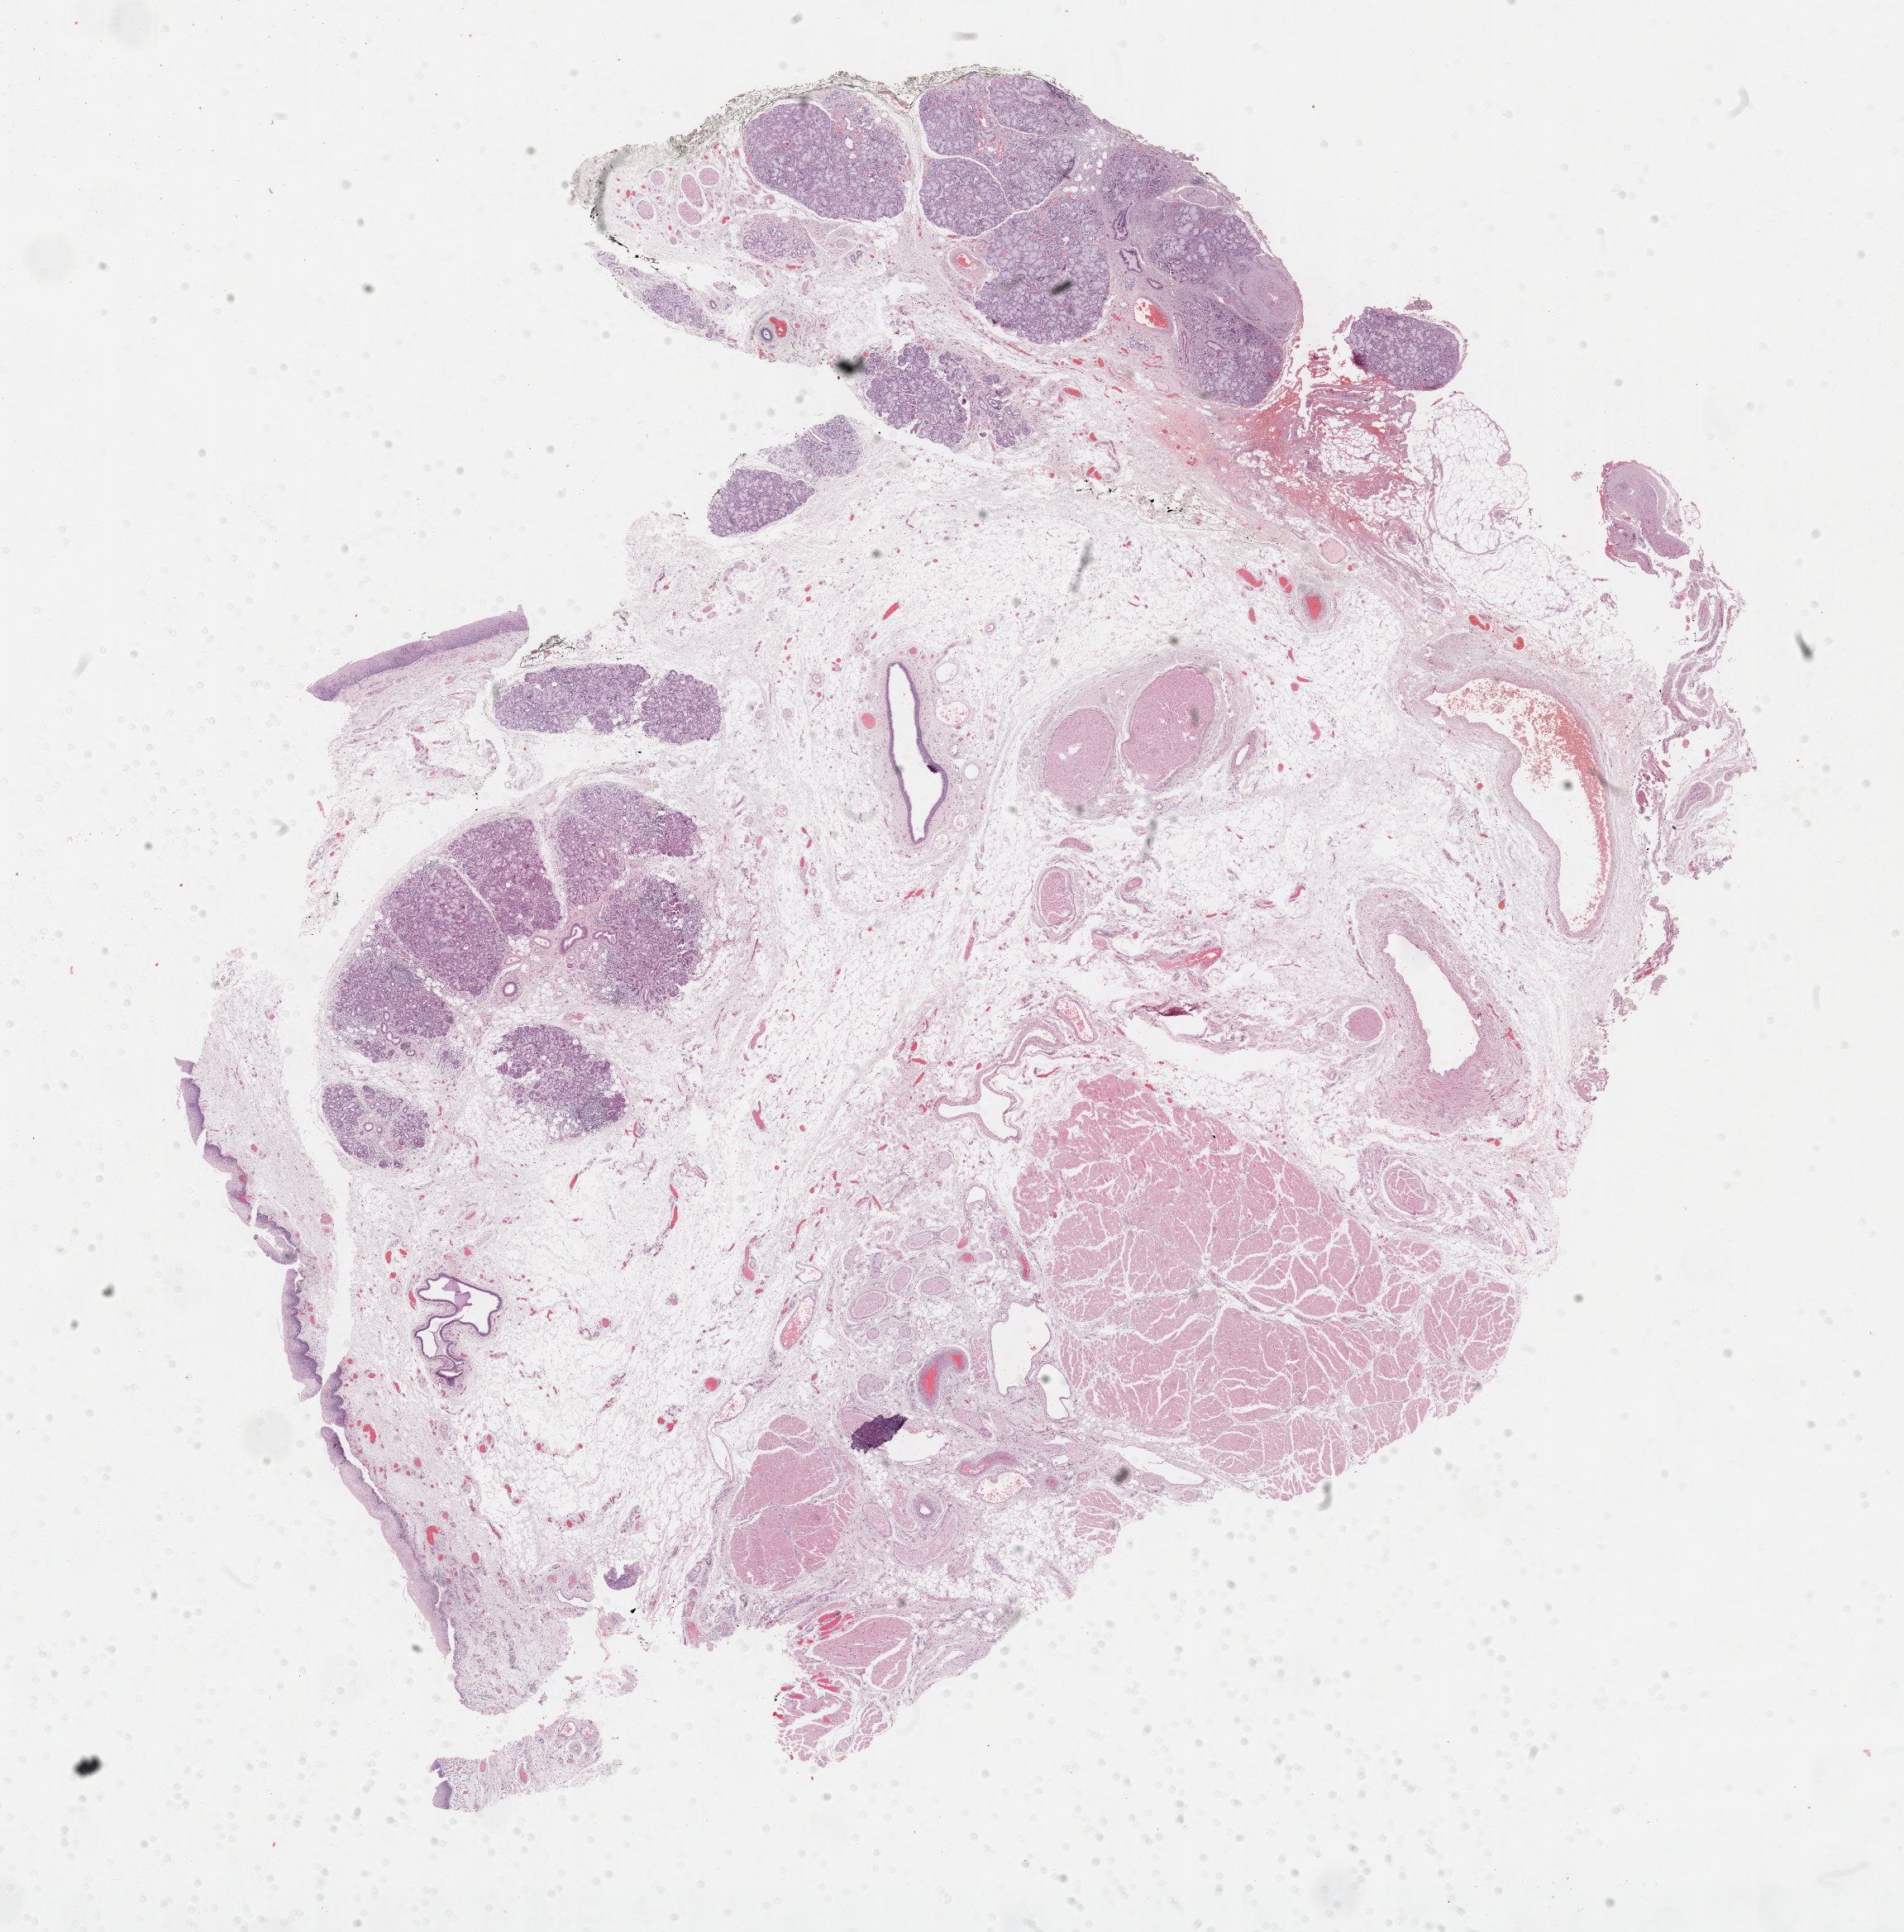
Hematoxylin and eosin (H&E) stained whole-slide image, shown as a low-resolution overview of the whole scanned area (about 18.6 x 18.9 mm); FFPE section; head and neck, primary tumour sample. Female patient; age at initial diagnosis 65 years. Histologic grade: G2 (moderately differentiated).
Laterality: left. Histologic diagnosis: Squamous cell carcinoma, NOS. Lymph nodes positive (case pathology): 1 of 17 examined. AJCC pathologic stage: III.